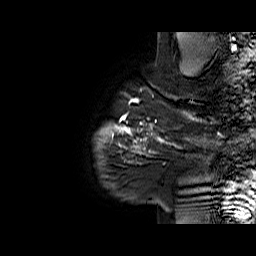
Breast MRI (dynamic contrast-enhanced), one sagittal slice. Slice 58 of 60 in the series (ordered by position). Dynamic contrast-enhanced series, time point 2 of 6 at this slice position (early post-contrast). 1.5 T. TE 6.1 ms, TR 32.9 ms. 256 × 256 image matrix, field of view 220 × 220 mm. Female patient. From the clinical record (not read from this slice): setting: breast cancer imaged before/during neoadjuvant chemotherapy; receptor status: HER2-positive.
Structures marked on this image (semi-automatic segmentation, software-assisted and operator-edited):
- analysis volume of interest (the breast-tissue region the enhancement analysis was run in; not a lesion): bounding box (x1, y1, x2, y2) in pixels: (127, 95, 194, 164)
- tumour enhancement mask (voxels above the 100 % enhancement threshold inside the analysis volume of interest): (127, 95, 194, 155)